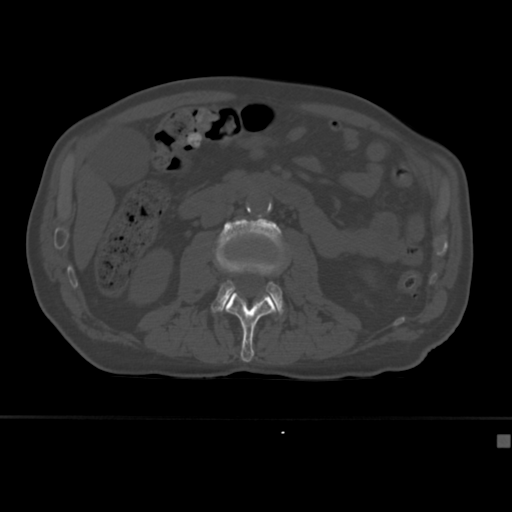
CT including the spine, one axial slice; position 139 of 430 along the scan axis; reconstruction kernel Br40s; bone window (W 1800 / L 400 HU); 1.5 mm slice thickness; 512 × 512 image matrix, field of view 337 × 337 mm. Male patient, age 64 years. From the clinical record (not read from this slice): primary cancer: uterus; vertebrae with lytic lesions (as recorded): T1, T4, T5, T7, L5.
Outlined on this slice (semi-automatic segmentation, software-assisted and operator-edited):
- L2 vertebra: bounding box (x1, y1, x2, y2) in pixels: (224, 292, 275, 362)
- L3 vertebra: (211, 218, 284, 314)